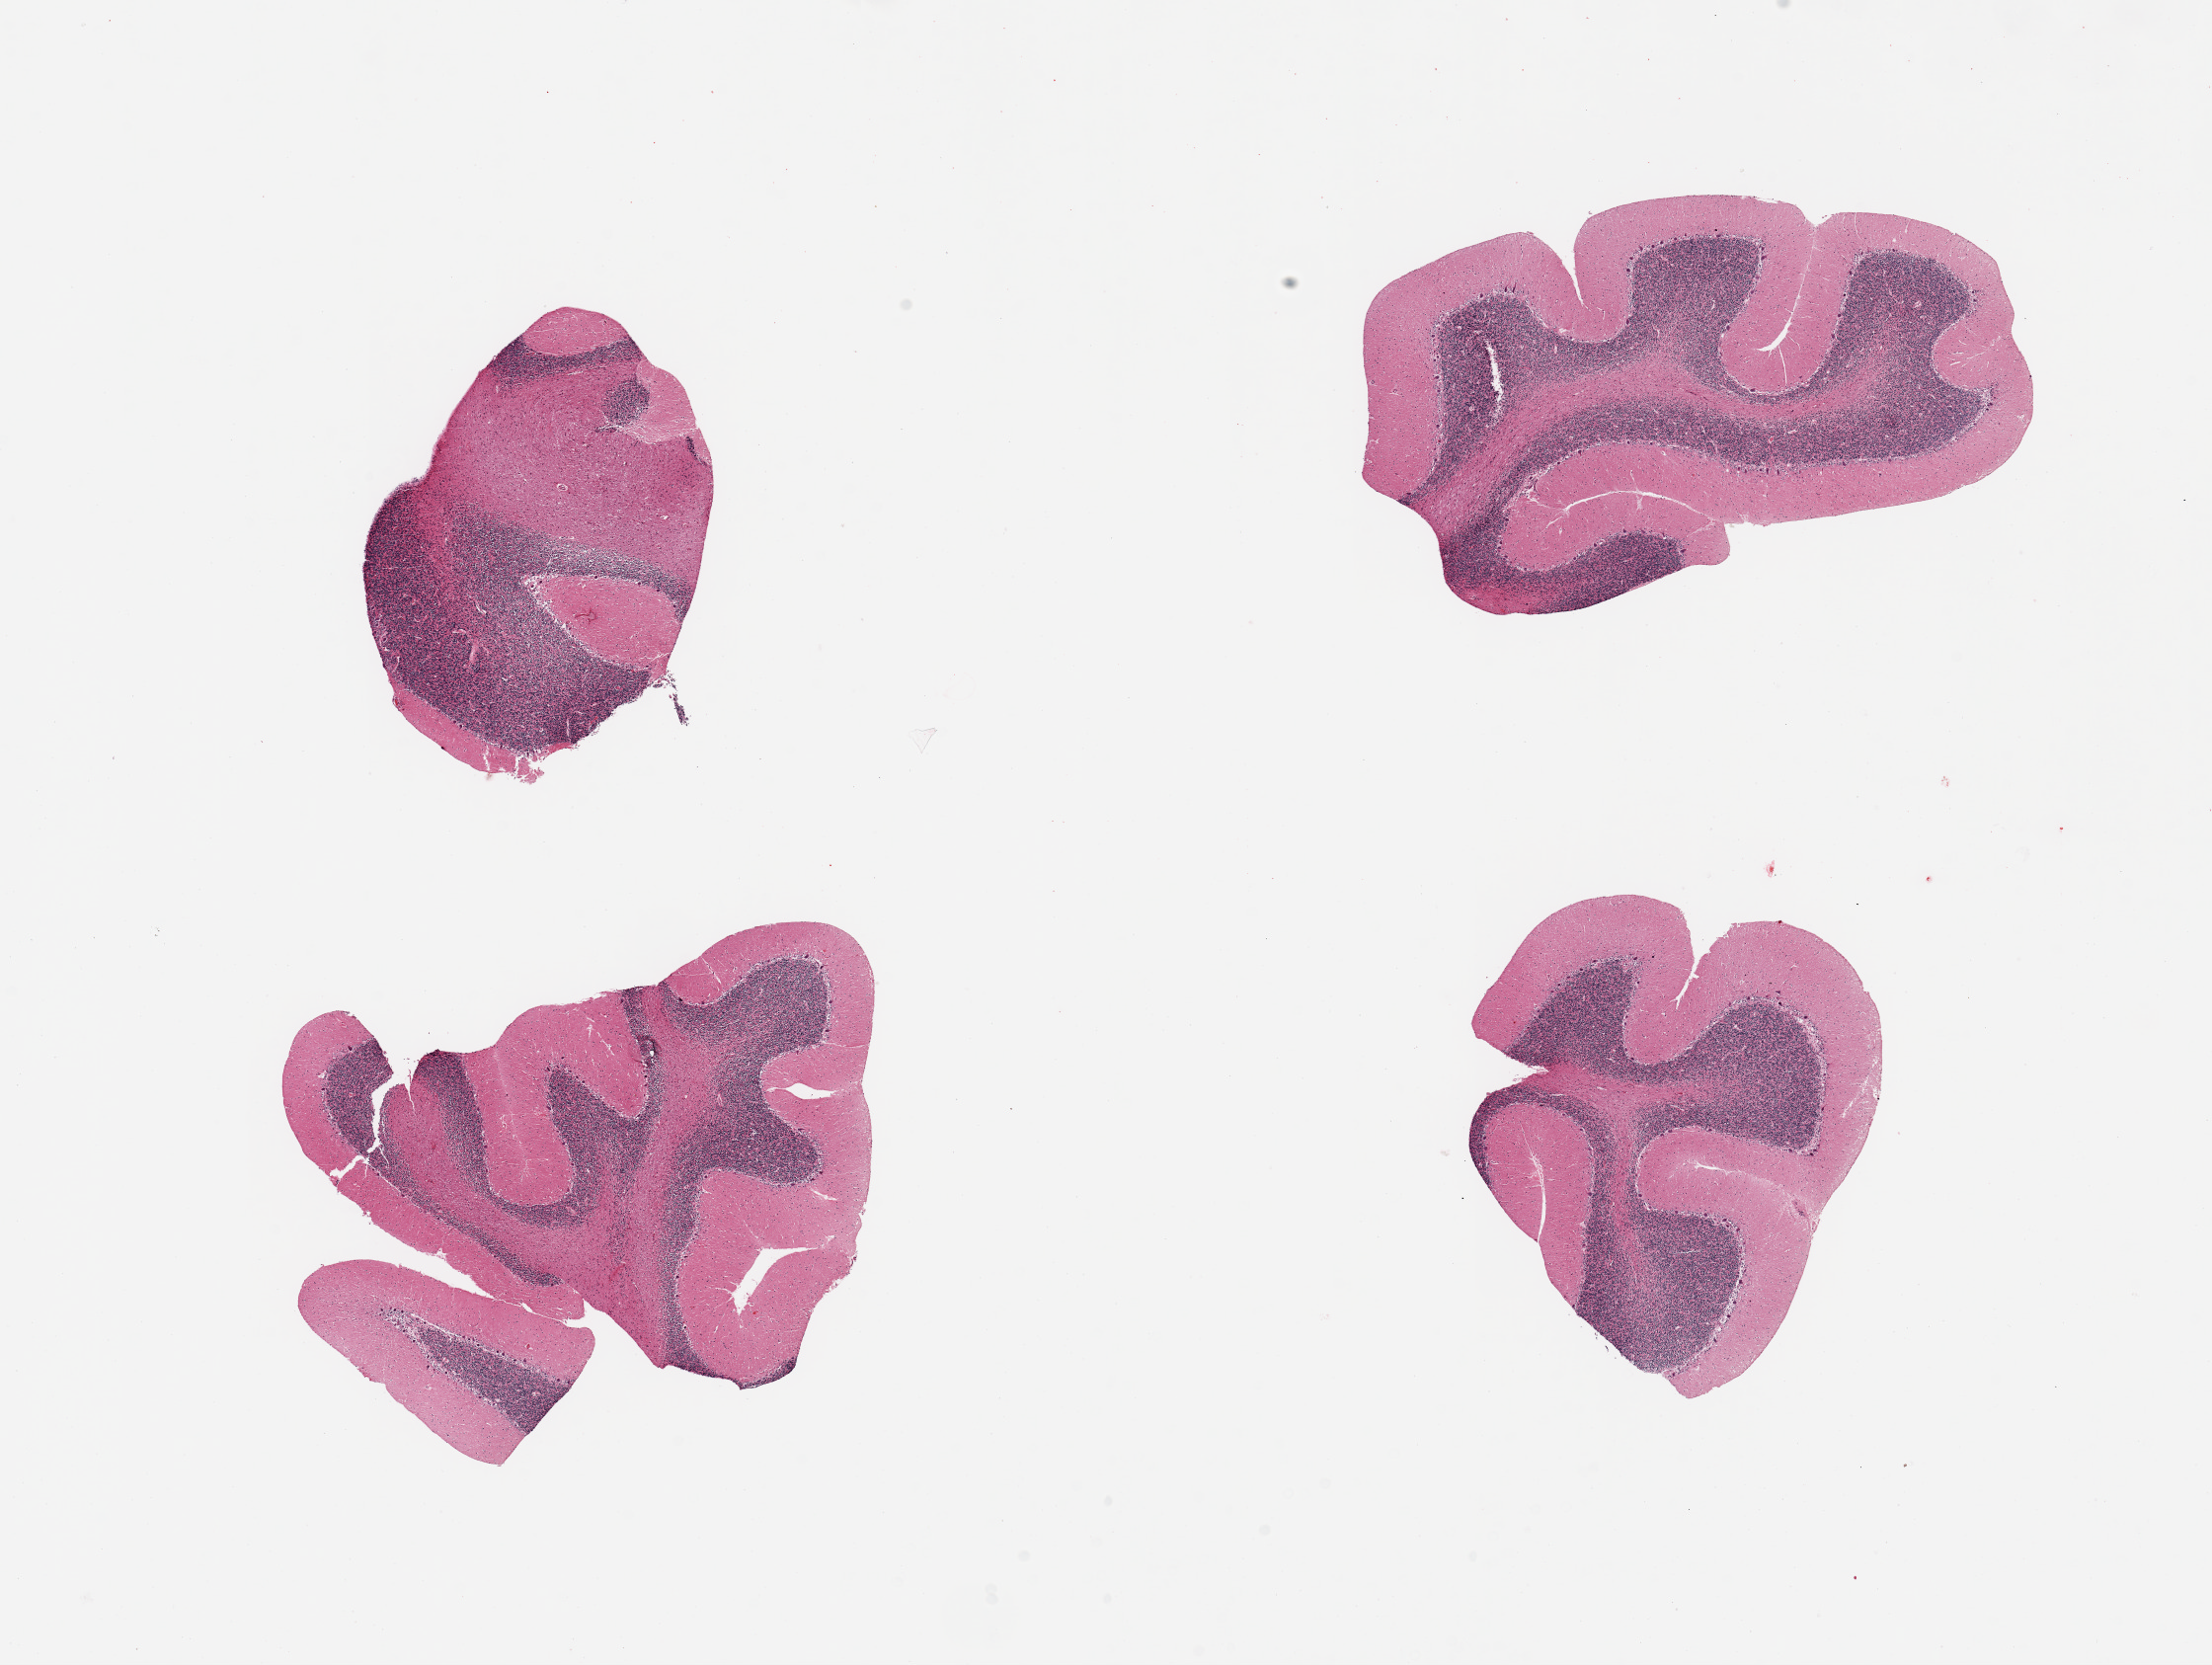
Whole-slide image, H&E stain — shown as a low-resolution overview of the whole scanned area (about 17.7 x 13.3 mm), PAXgene-fixed, paraffin-embedded tissue, section of cerebellum (target tissue), donor tissue sample. Donor sex: female.
• reviewer comment on this tissue sample: 4 pieces